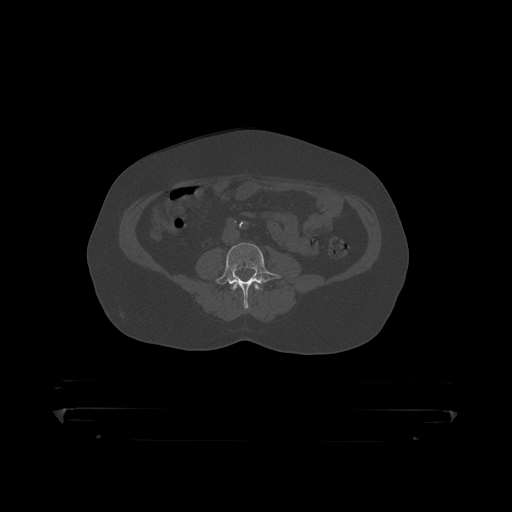
CT including the spine, one axial slice; slice 67 of 390 in the series (ordered by position); reconstruction kernel STANDARD; bone window (W 1800 / L 400 HU); 512 × 512 image matrix. Patient: male, 60 years. From the clinical record (not read from this slice): primary cancer: prostate.
Annotated regions visible in this slice (semi-automatic segmentation, software-assisted and operator-edited):
- L3 vertebra: bounding box <231,283,263,292> (left, top, right, bottom; pixels)
- L4 vertebra: <214,243,282,310>